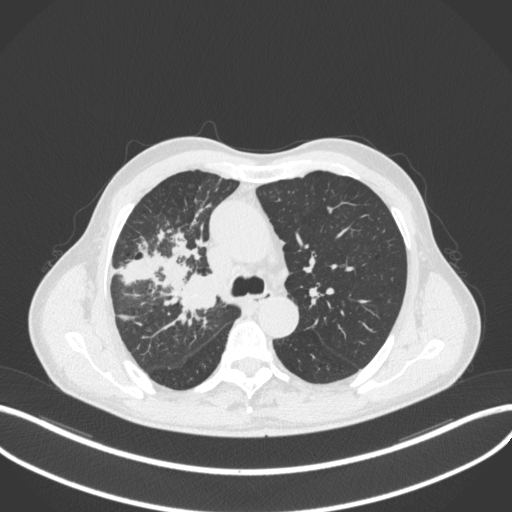
Chest CT, one axial slice. Position 329 of 490 along the scan axis. Reconstruction kernel B31f. Lung window (W 1500 / L -600 HU). 1 mm slice thickness. 512 × 512 image matrix. Patient: male, 69 years. Case-level facts recorded for this patient, not image findings: clinical TNM (as recorded): T2a N0 M0.
Outlined on this slice (rectangle marked by the reading radiologist):
- lung tumour (recorded histology: adenocarcinoma): bounding box <173,271,218,313> (left, top, right, bottom; pixels)